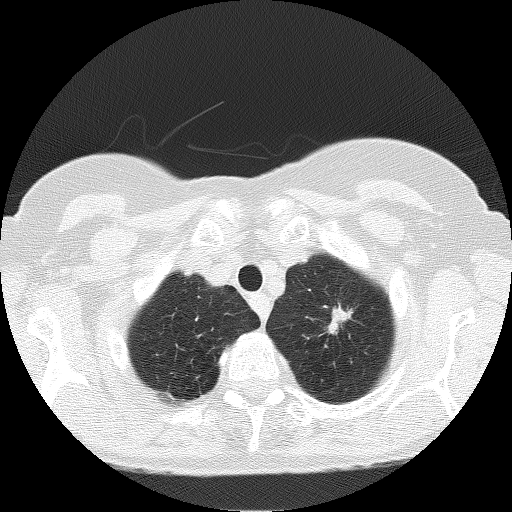
Chest CT (low-dose screening protocol), one axial image, baseline annual screen, lung window (W 1500 / L -600 HU), 512 × 512 image matrix. Female participant, aged 66 years at enrolment.
• Expert reader's lesion annotation, bounding box [x1, y1, x2, y2] px = [312, 285, 371, 351].
• The screening reader recorded 3 non-calcified nodules or masses ≥4 mm on this exam (left upper lobe, left upper lobe, left upper lobe); which of them this box marks is not recorded.
• Participant outcome: lung cancer diagnosed 156 days after this screen — adenocarcinoma, NOS, left upper lobe, moderately differentiated (G2), stage IB (AJCC 6th edition), 17 mm at pathology.